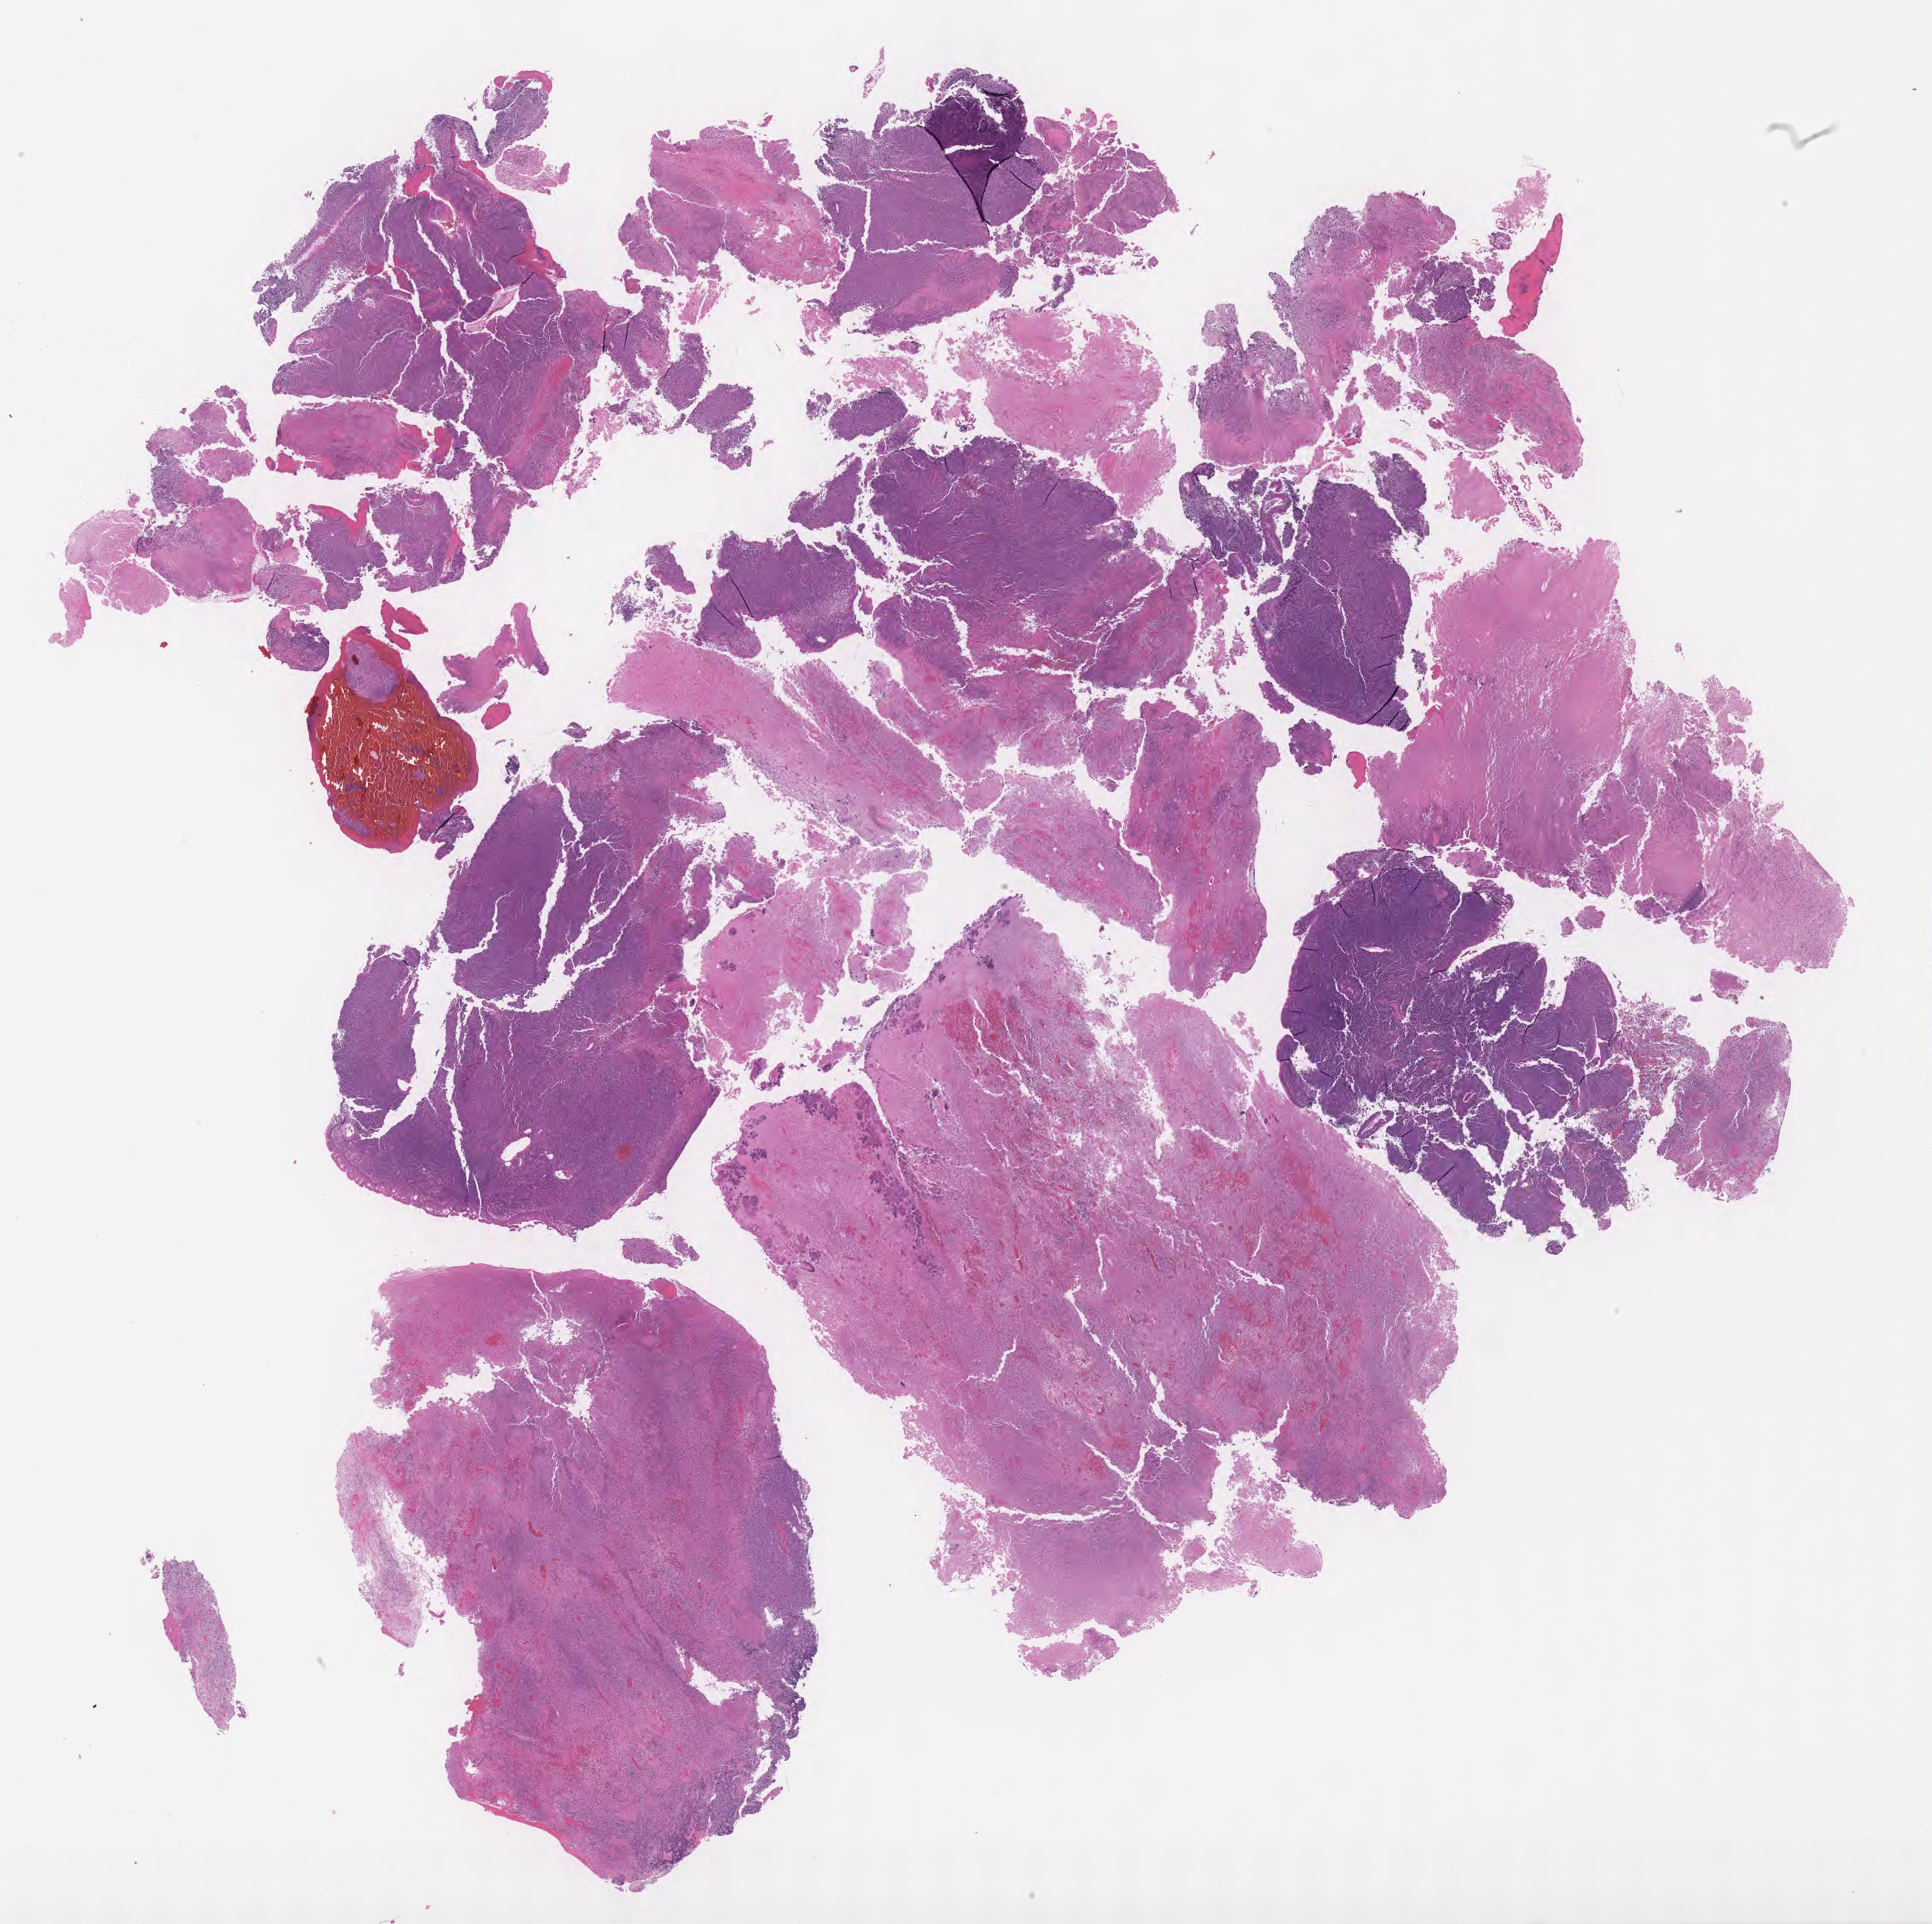
Digitized haematoxylin and eosin-stained section, whole scanned area (about 21.1 x 21.0 mm) shown as a low-resolution overview; tumor tissue. Patient: male, 47 years old.
- histologic diagnosis: Diffuse large B-cell lymphoma, NOS